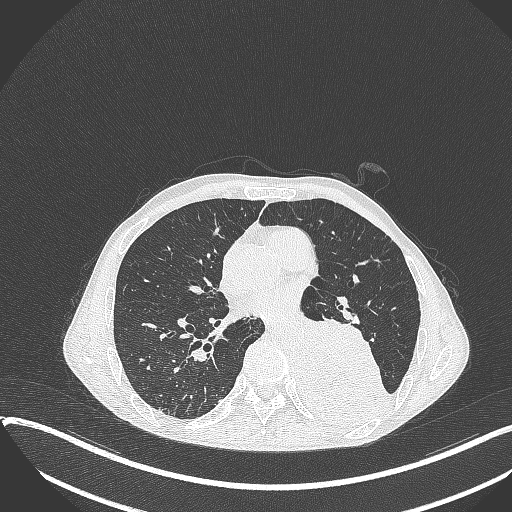
Chest CT, one axial slice; position 172 of 401 along the scan axis; lung window (W 1500 / L -600 HU); 1 mm slice thickness; 512 × 512 image matrix, field of view 400 × 400 mm. Male patient, age 57 years. From the clinical record (not read from this slice): clinical TNM (as recorded): T4 N0 M0.
Structures marked on this image (rectangle marked by the reading radiologist):
- lung tumour (recorded histology: squamous cell carcinoma): bounding box (x1, y1, x2, y2) in pixels: (294, 307, 401, 432)